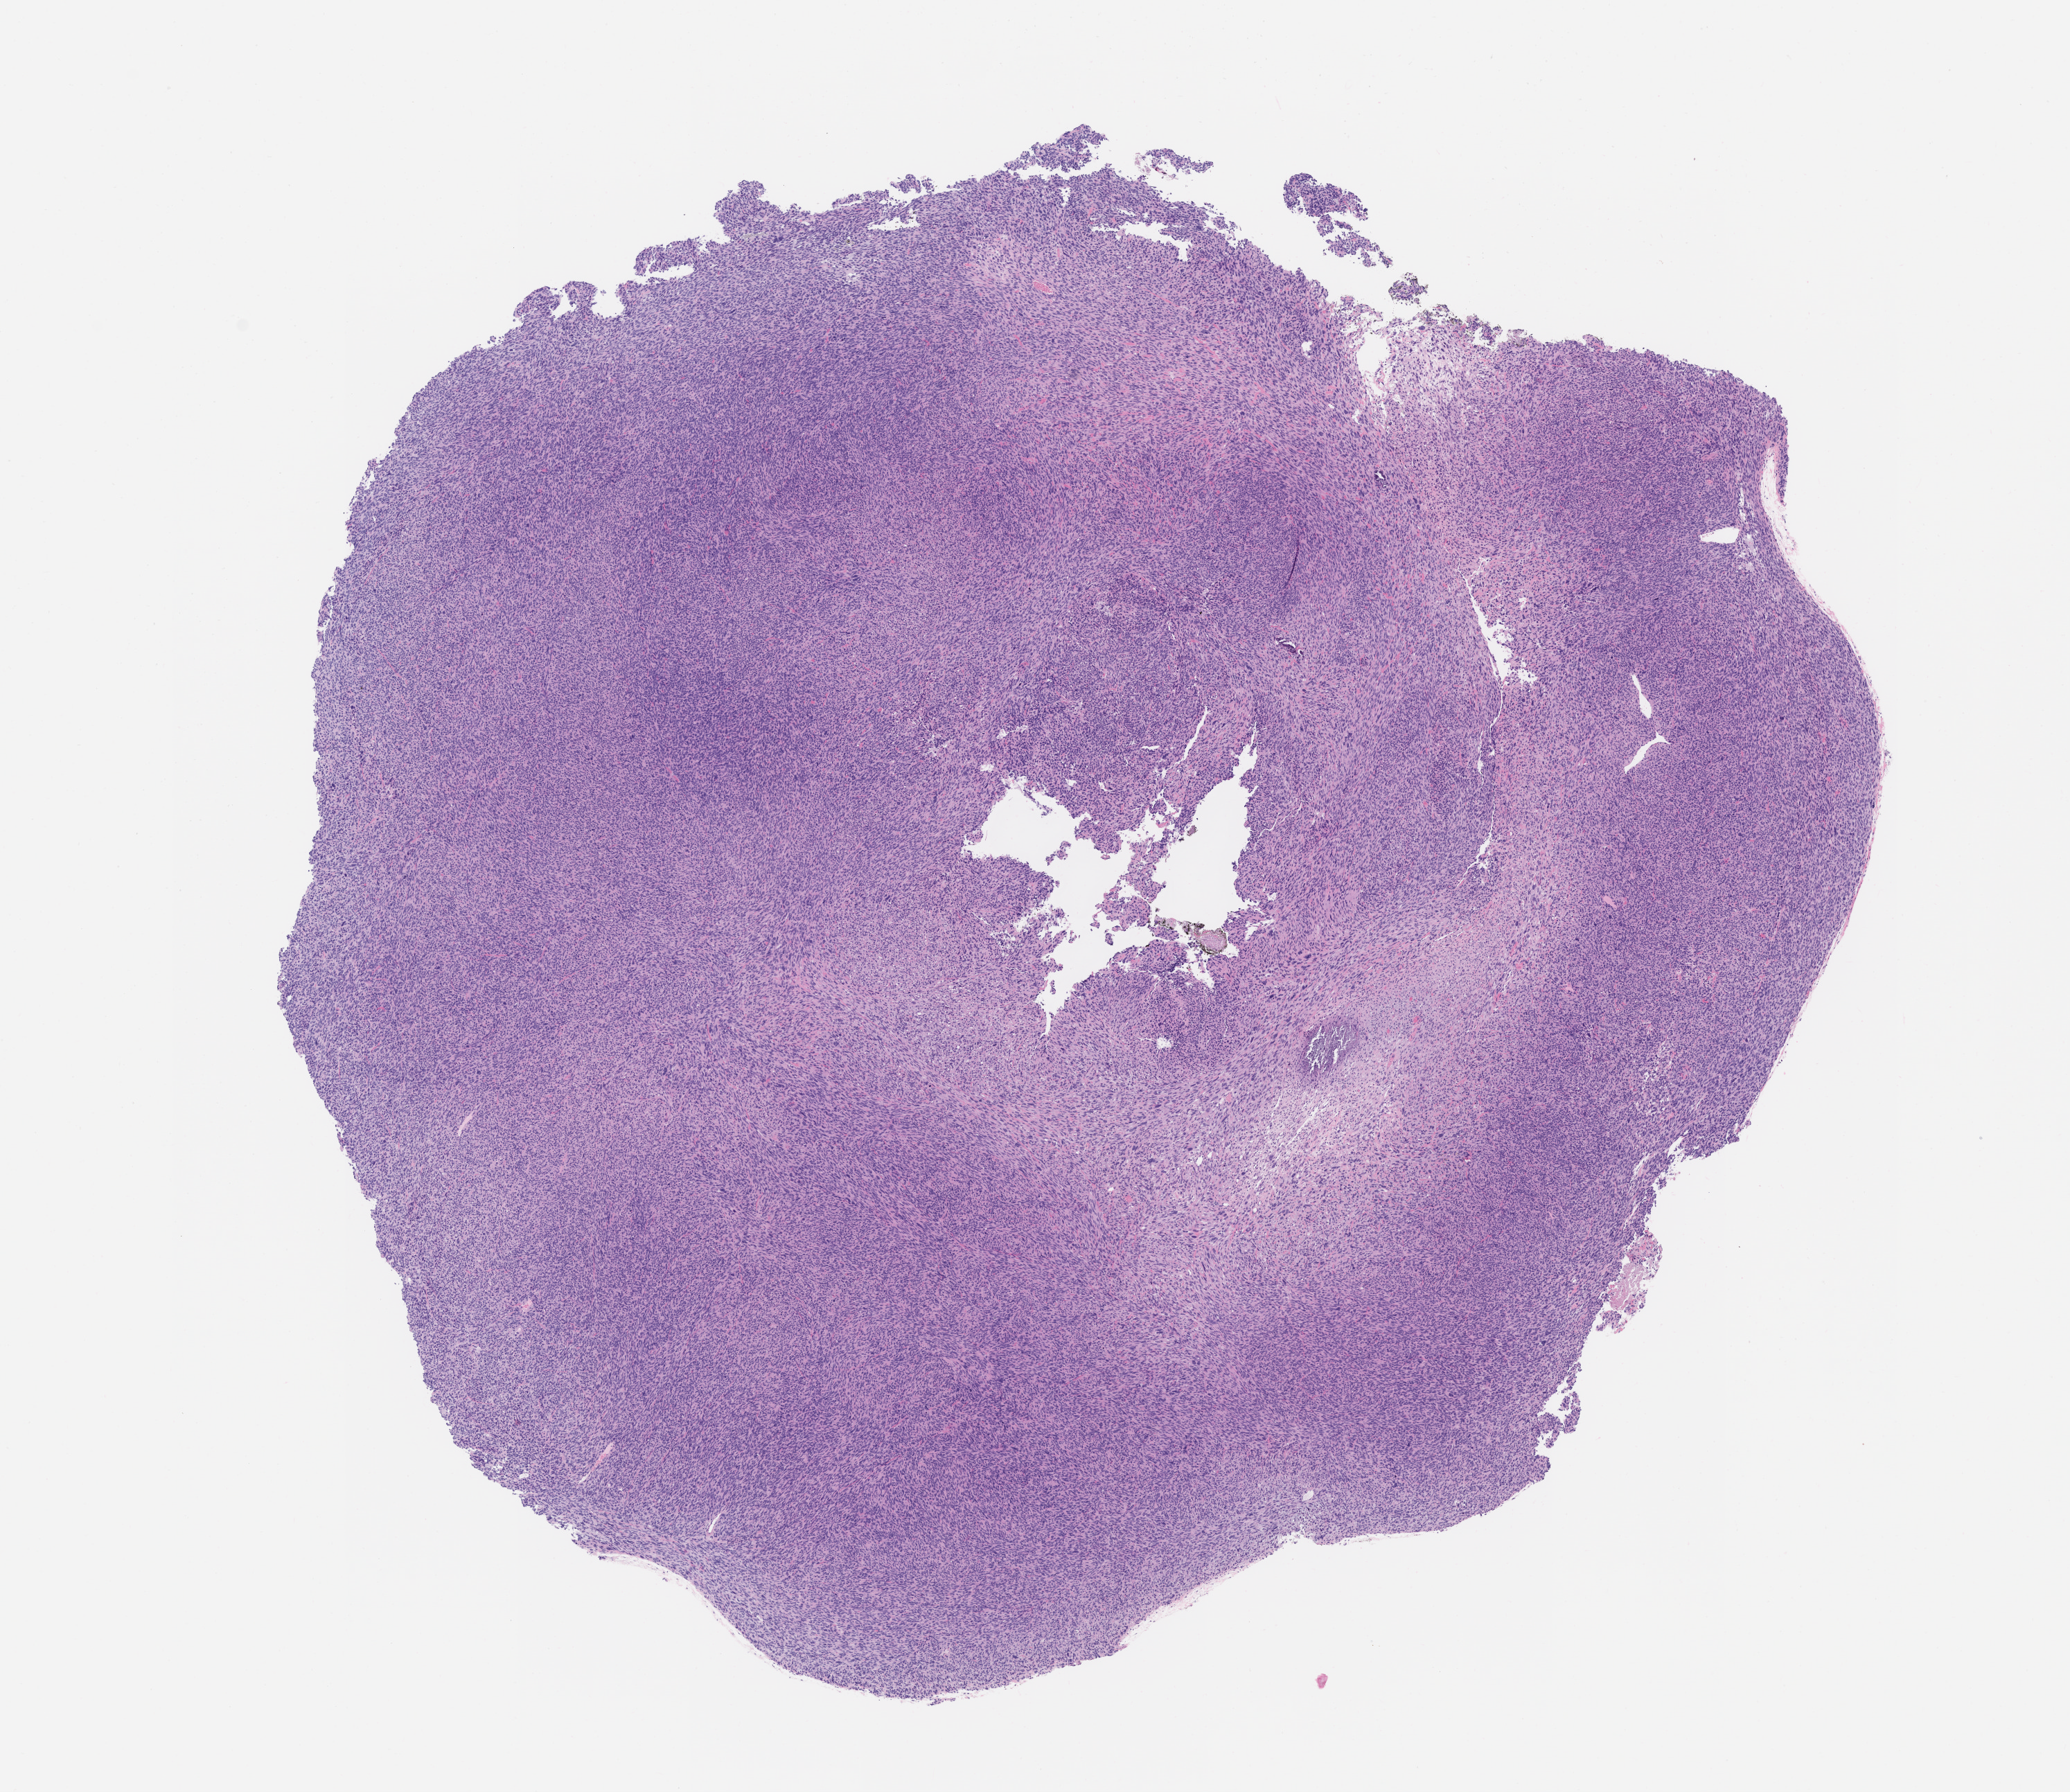
Whole-slide image, hematoxylin and eosin (H&E): patient-derived xenograft (human tumor grown in a mouse), passage 3, shown as a low-resolution overview of the whole scanned area (about 12.0 x 10.4 mm), FFPE section, tumor site category: uterus.
• originating patient diagnosis: Leiomyosarcoma